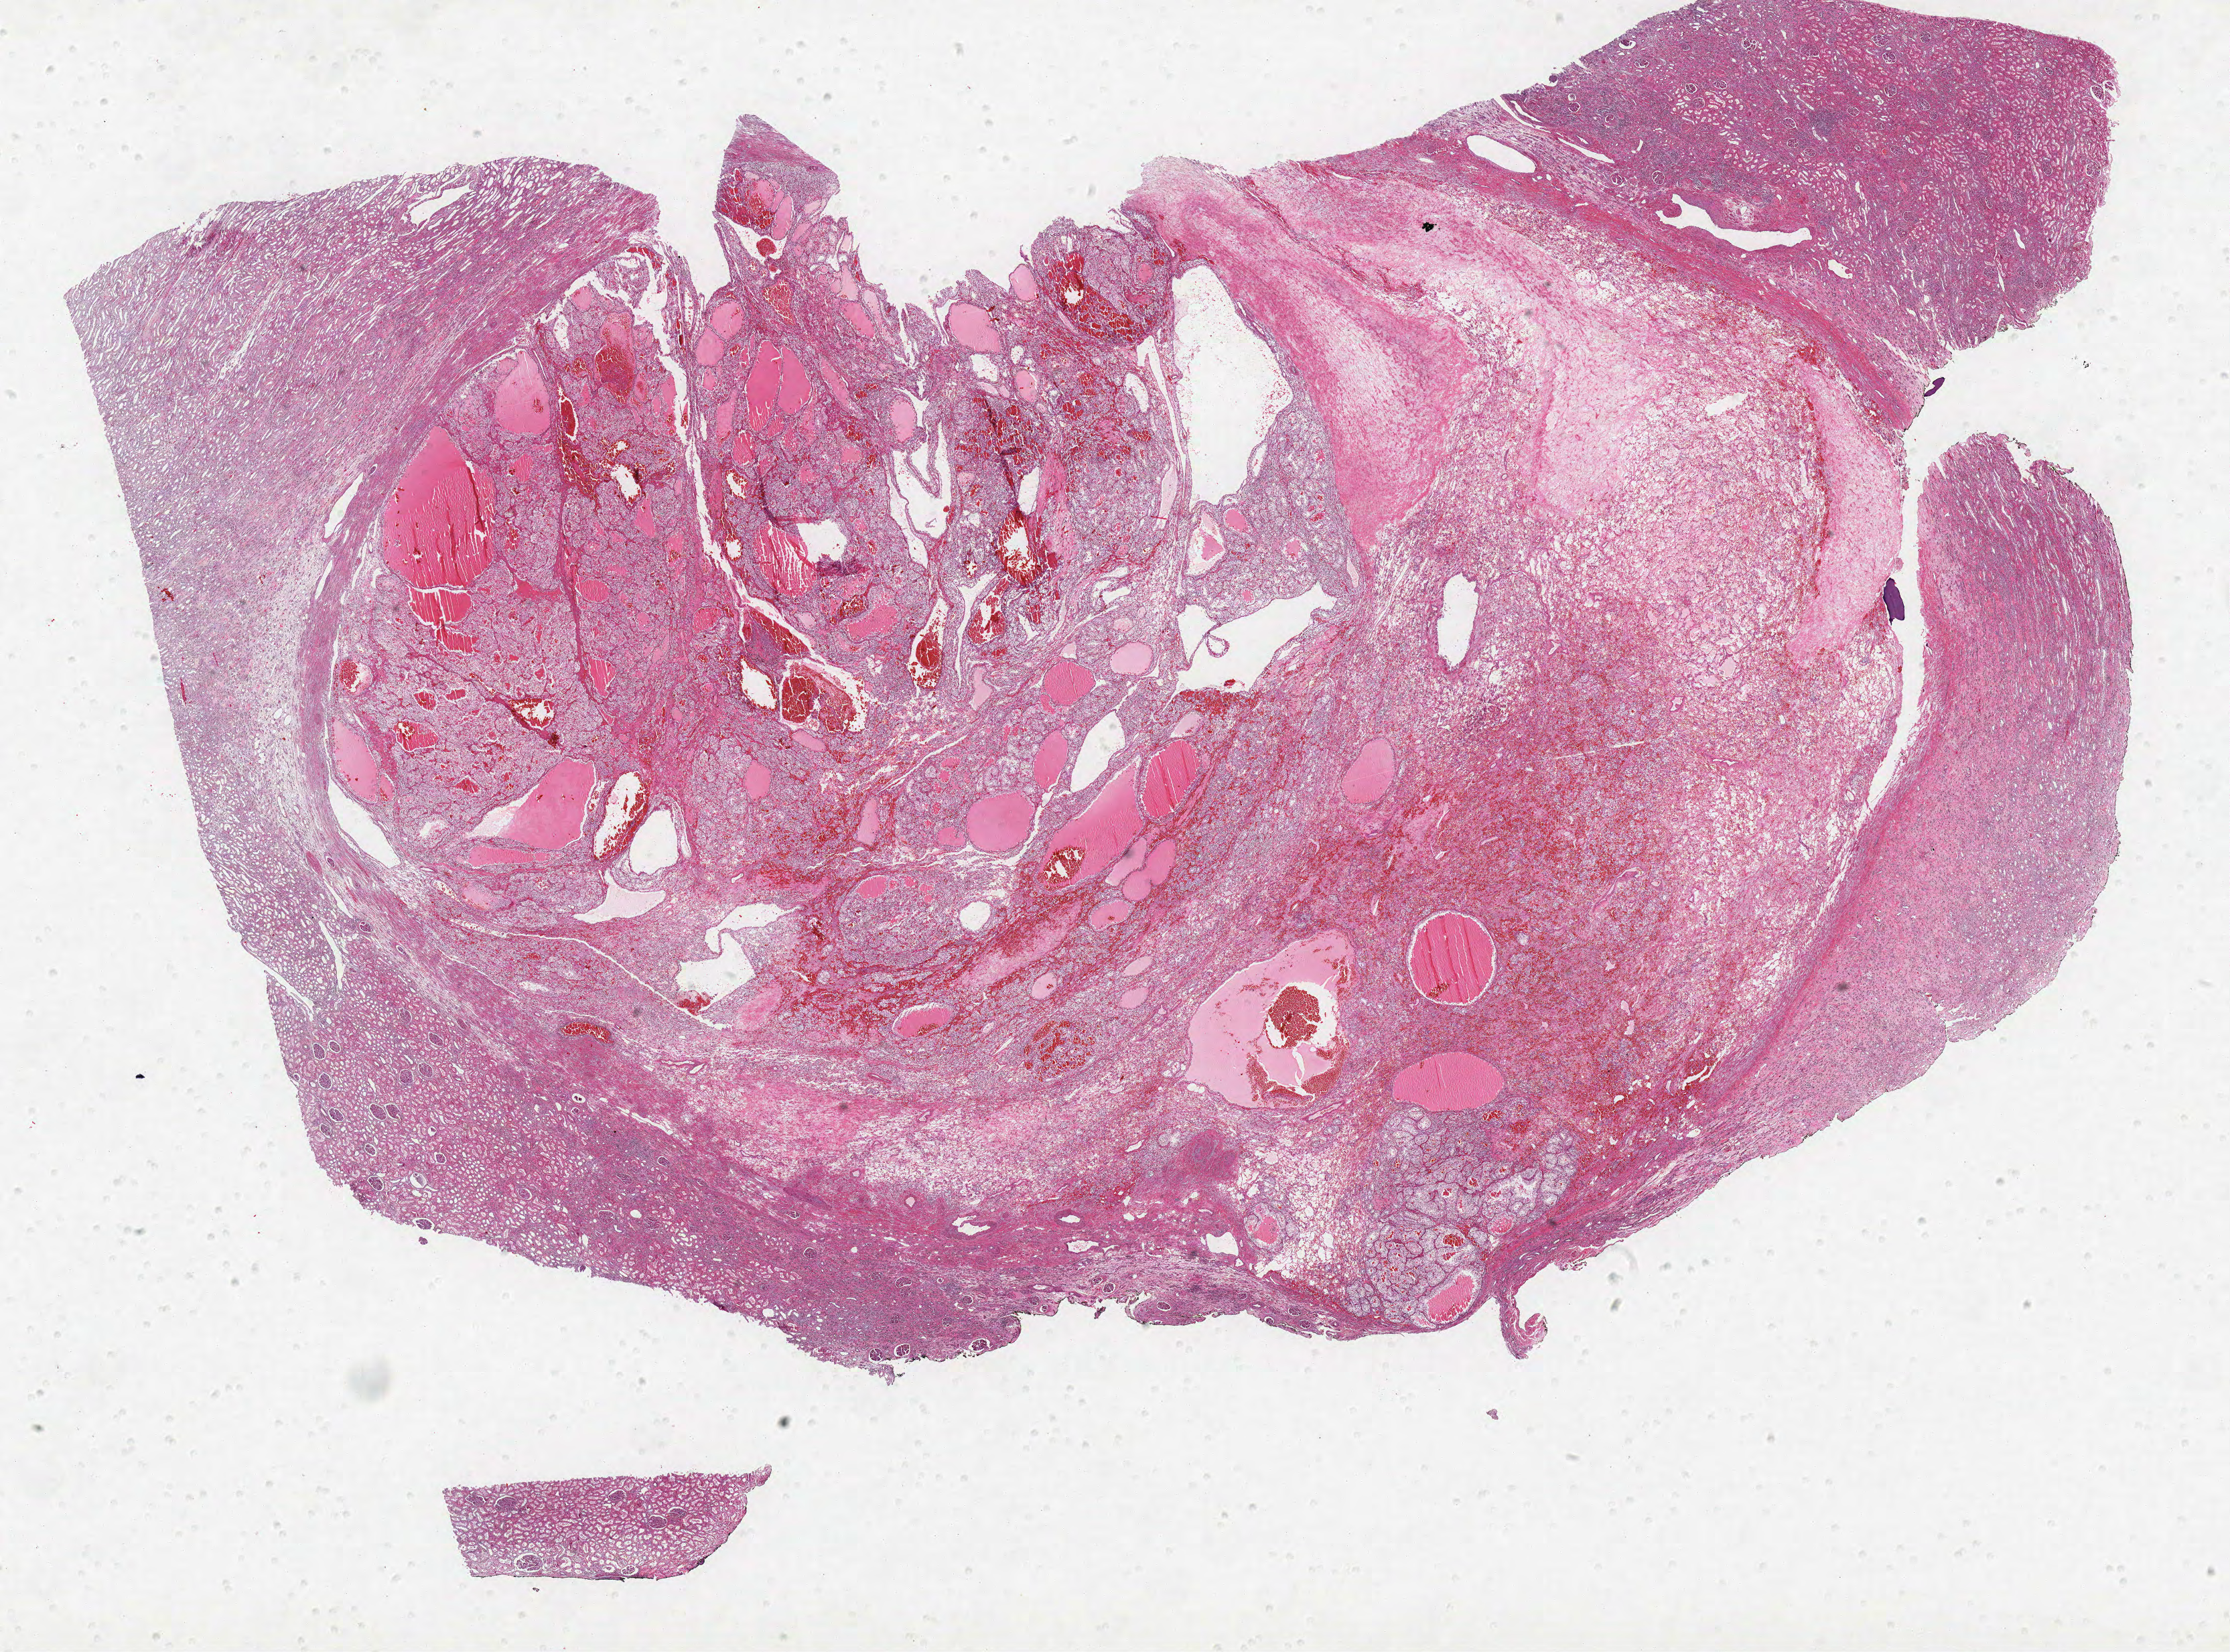
H&E whole-slide image, whole scanned area (about 26.6 x 19.7 mm, slide scanned at 40x) shown as a low-resolution overview; formalin-fixed paraffin-embedded (FFPE) diagnostic section; kidney, primary tumour sample. Male patient; age at initial diagnosis 58 years. Histologic grade: G3 (poorly differentiated).
Laterality: left. AJCC pathologic stage: I. Diagnosis: Clear cell adenocarcinoma, NOS.